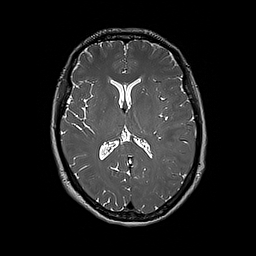
Brain MRI from a brain-tumour surgery series, one axial slice. Slice 97 of 192 in the series (ordered by position). 1 mm slice thickness. 256 × 256 image matrix, field of view 250 × 250 mm. Case-level facts recorded for this patient, not image findings: histopathology: Glioblastoma; WHO grade: 4; IDH mutation: no; tumour location: Left Frontal.
Structures marked on this image (expert manual segmentation):
- tumour: bounding box (x1, y1, x2, y2) in pixels: (182, 131, 189, 168)